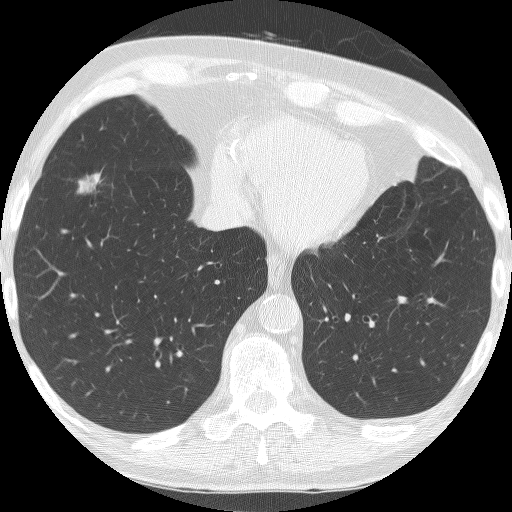
Low-dose screening chest CT, axial slice; first (baseline) screen; lung window (W 1500 / L -600 HU); lung (sharp) reconstruction kernel (BONE); 512 × 512 image matrix, field of view 320 × 320 mm. Male, age 74 years at enrolment. Former smoker at enrolment.
Lesion marked by an expert reader, bounding box (x1, y1, x2, y2) in pixels: (67, 163, 120, 206). The screening reader recorded 4 non-calcified nodules or masses ≥4 mm on this exam; which of them this box marks is not recorded. Lung cancer was diagnosed 35 days after this screen: bronchiolo-alveolar carcinoma, mucinous, right lower lobe, well differentiated (G1), stage IA (AJCC 6th edition), 22 mm at pathology.